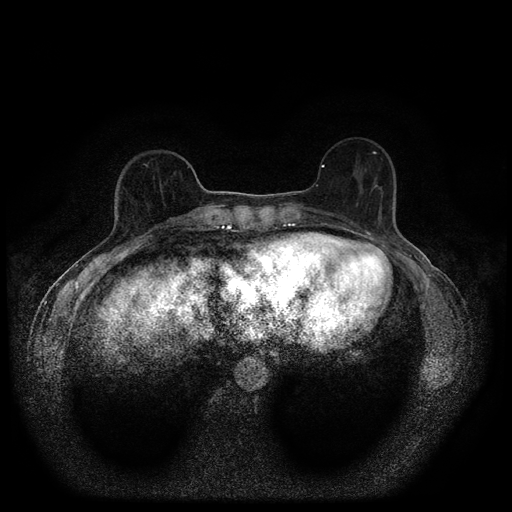
Breast MRI (dynamic contrast-enhanced, multi-phase), one axial slice; position 32 of 116 along the scan axis; dynamic contrast-enhanced series, time point 2 of 5 at this slice position (early post-contrast); 1.5 T; TE 2.7 ms, TR 5.4 ms; 512 × 512 image matrix, field of view 330 × 330 mm. Female patient, age 56 years.
Outlined on this slice (semi-automatic segmentation, software-assisted and operator-edited):
- breast lesion (labelled 'tumour' in the annotation; benign lesions carry a separate 'benign' label): bounding box (x1, y1, x2, y2) in pixels: (371, 178, 380, 191)